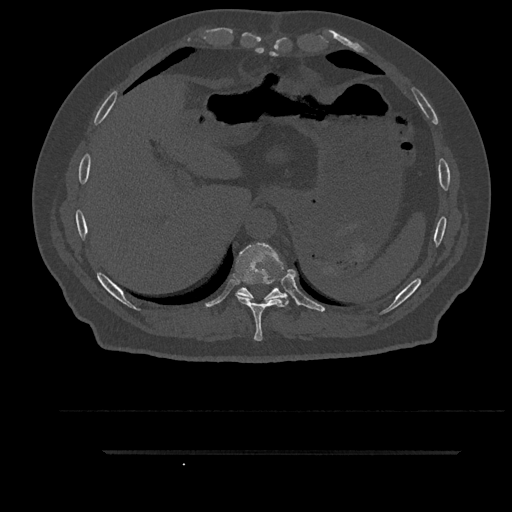
CT including the spine, one axial slice. Position 399 of 797 along the scan axis. Bone window (W 1800 / L 400 HU). 0.5 mm slice thickness. 512 × 512 image matrix, field of view 432 × 432 mm. Male patient, age 63 years. Case-level facts recorded for this patient, not image findings: primary cancer: renal.
Outlined on this slice (semi-automatic segmentation, software-assisted and operator-edited):
- T10 vertebra: bounding box <236,287,288,302> (left, top, right, bottom; pixels)
- T9 vertebra: <234,243,289,341>